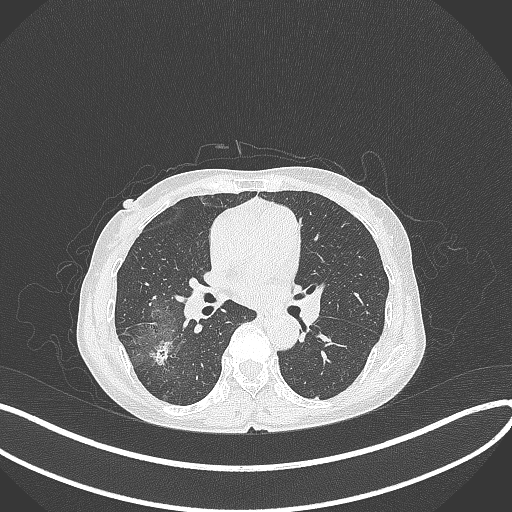
Chest CT, one axial slice. Slice 209 of 371 in the series (ordered by position). Reconstruction kernel B70f. 120 kVp. Lung window (W 1500 / L -600 HU). 1 mm slice thickness. 512 × 512 image matrix, field of view 400 × 400 mm. Patient: female, 69 years. From the clinical record (not read from this slice): clinical TNM (as recorded): T1b N0 M0.
Structures marked on this image (rectangle marked by the reading radiologist):
- lung tumour (recorded histology: adenocarcinoma): box from (x=144, y=334) to (x=176, y=371) px